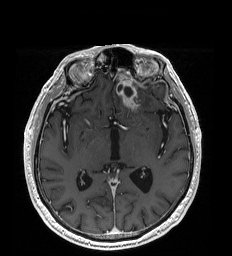
Brain MRI from a brain-tumour surgery series, one axial slice. Position 108 of 192 along the scan axis. T1-weighted post-contrast. 1 mm slice thickness. 232 × 256 image matrix. Case-level facts recorded for this patient, not image findings: histopathology: Glioblastoma; WHO grade: 4; IDH mutation: no.
Structures marked on this image (outlined manually by an expert reader):
- tumour: box from (x=117, y=86) to (x=138, y=110) px